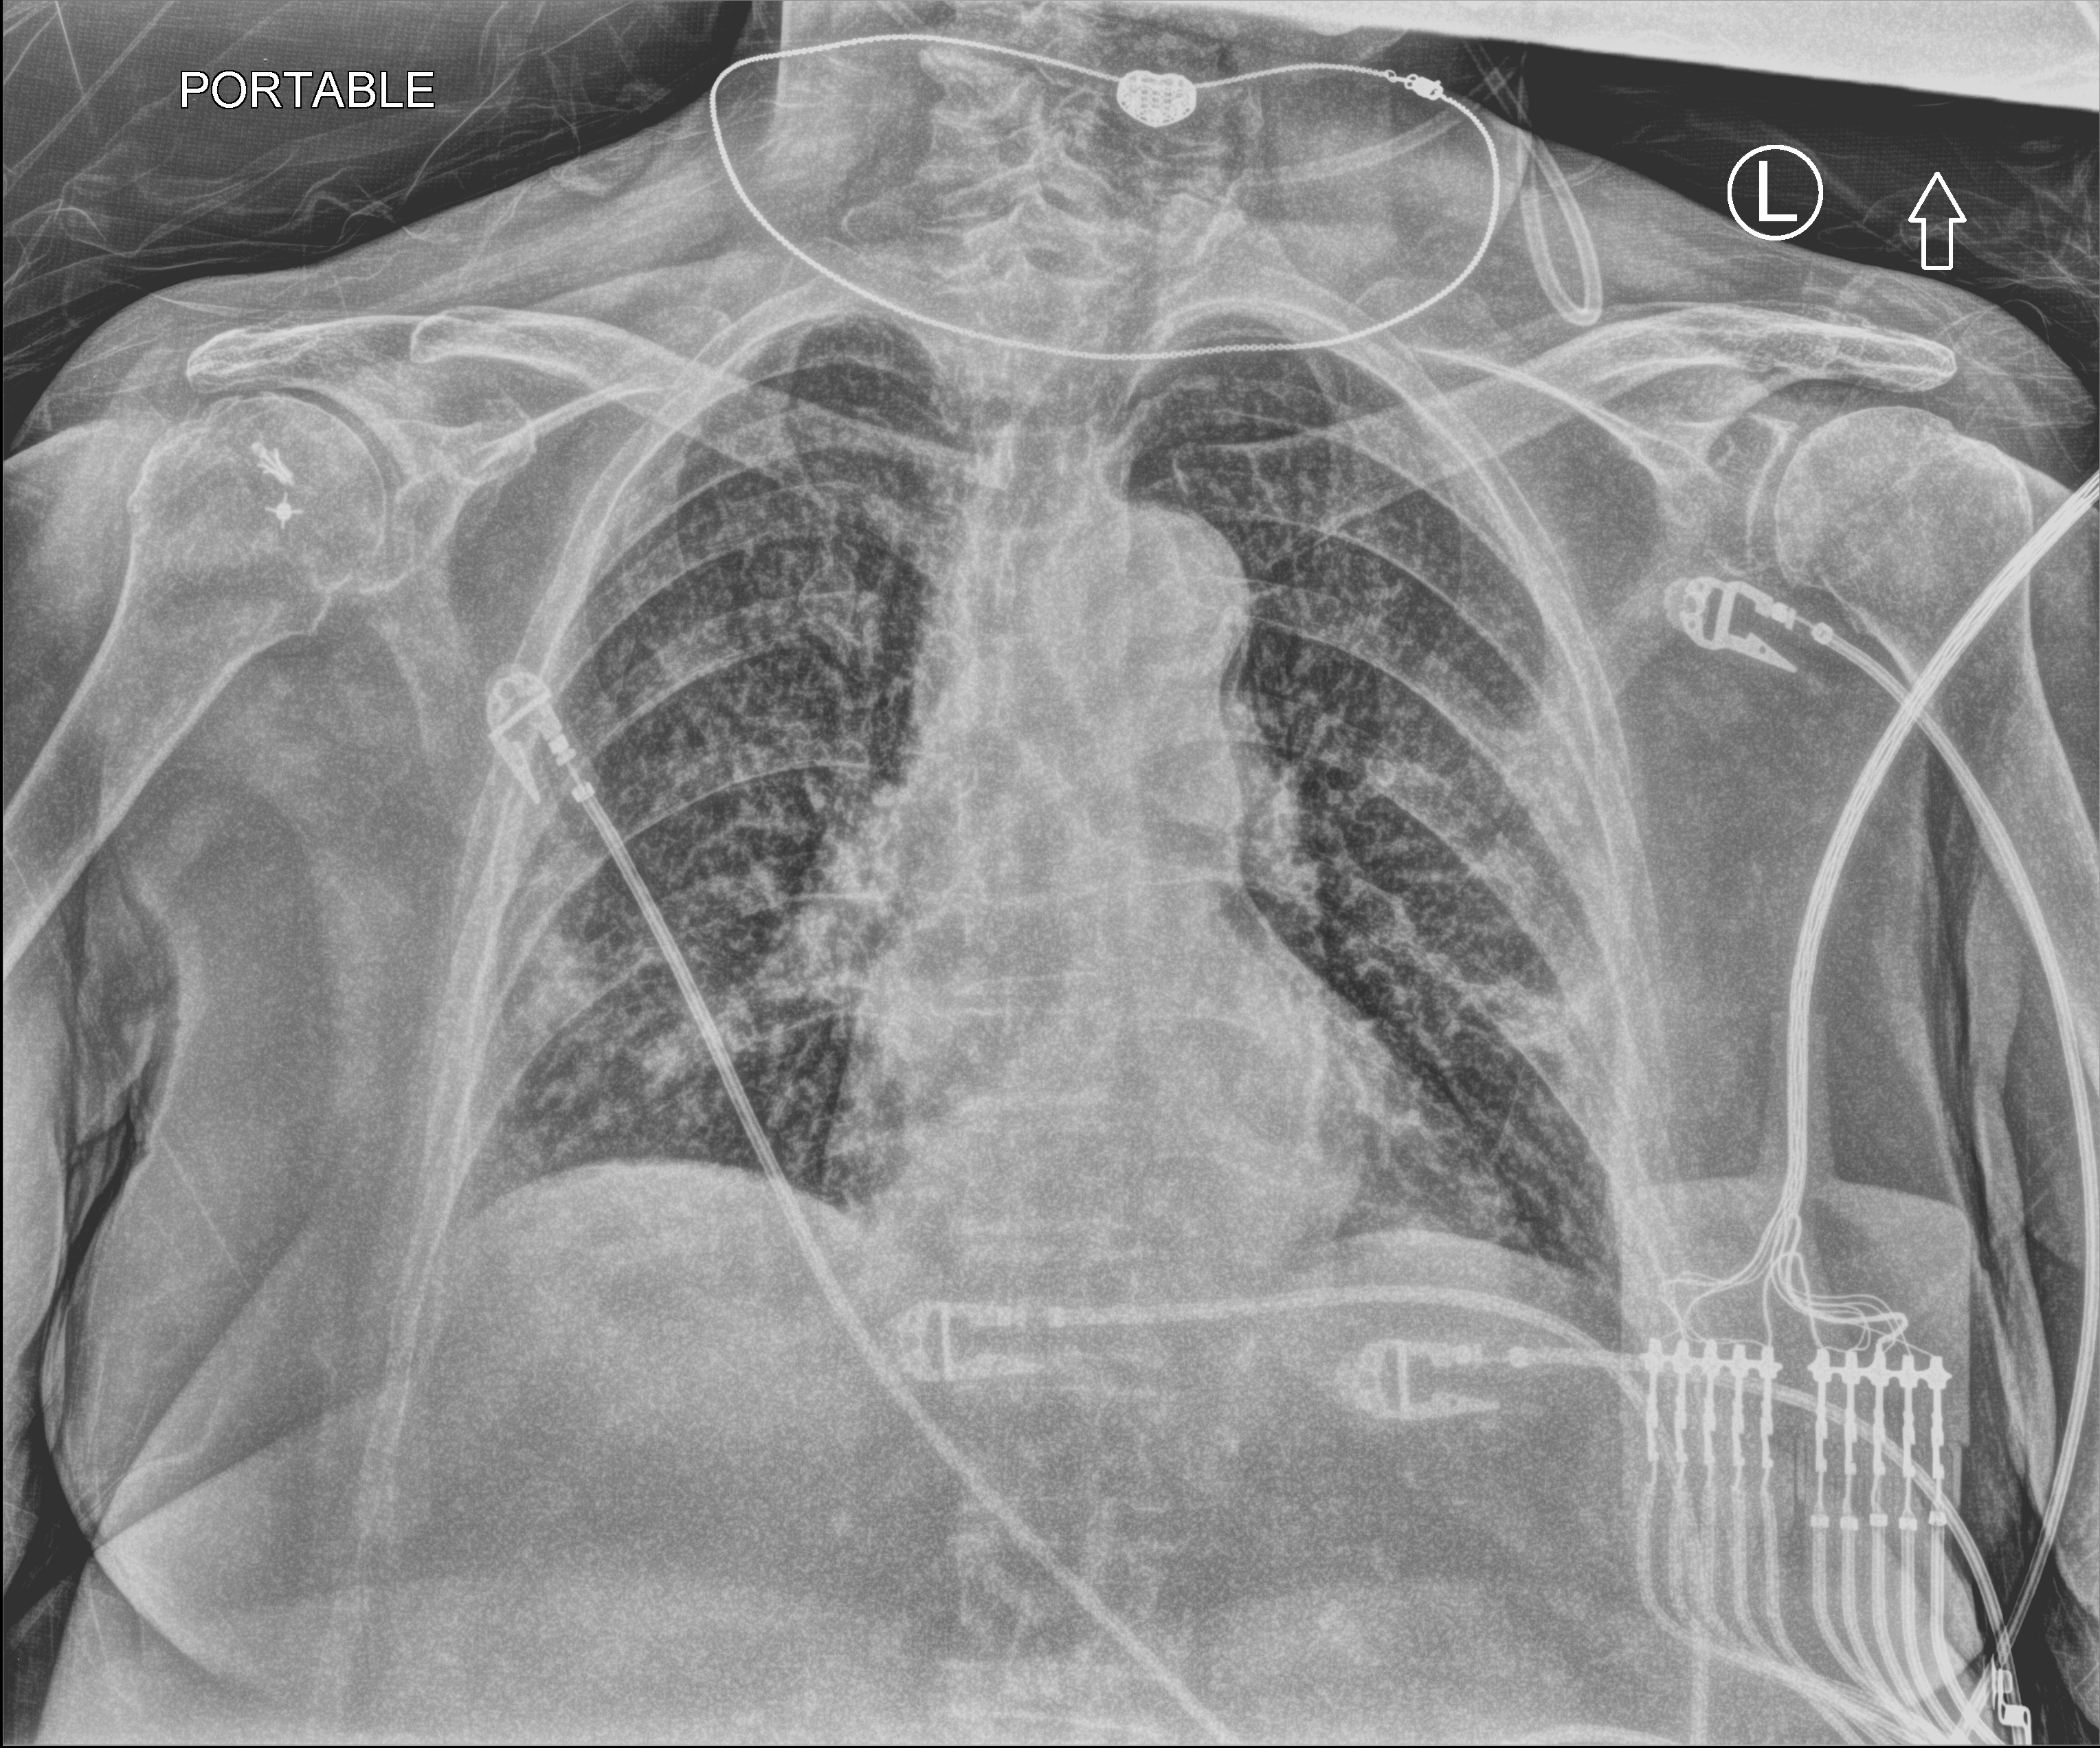
Portable chest radiograph; anteroposterior (AP) projection. Patient hospitalised with COVID-19; female, aged 75–90 years.
From the hospital-stay record, not from the radiograph (when in the stay this image was taken is not recorded): admitted to intensive care during this hospital stay: yes; length of hospital stay: 7 days.